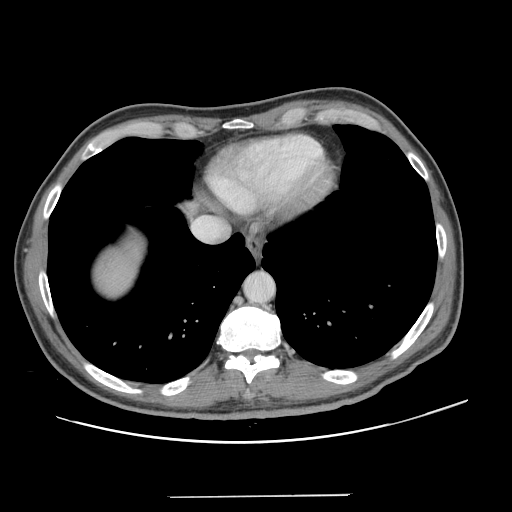
Contrast-enhanced abdominal CT, one axial slice. Slice 121 of 131 in the series (ordered by position). 120 kVp. Intravenous contrast given. Soft-tissue window (W 400 / L 40 HU). 2.5 mm slice thickness. 512 × 512 image matrix, field of view 403 × 403 mm. Male patient, age 60 years. From the clinical record (not read from this slice): diagnosis: colorectal cancer liver metastases, imaged before liver resection; multiple liver metastases: no; largest metastasis: 2.5 cm.
Structures marked on this image (outlined manually by an expert reader):
- liver: bounding box [x1, y1, x2, y2] px = [97, 246, 139, 297]
- planned liver remnant (the part of the liver to remain after resection): [97, 246, 138, 297]